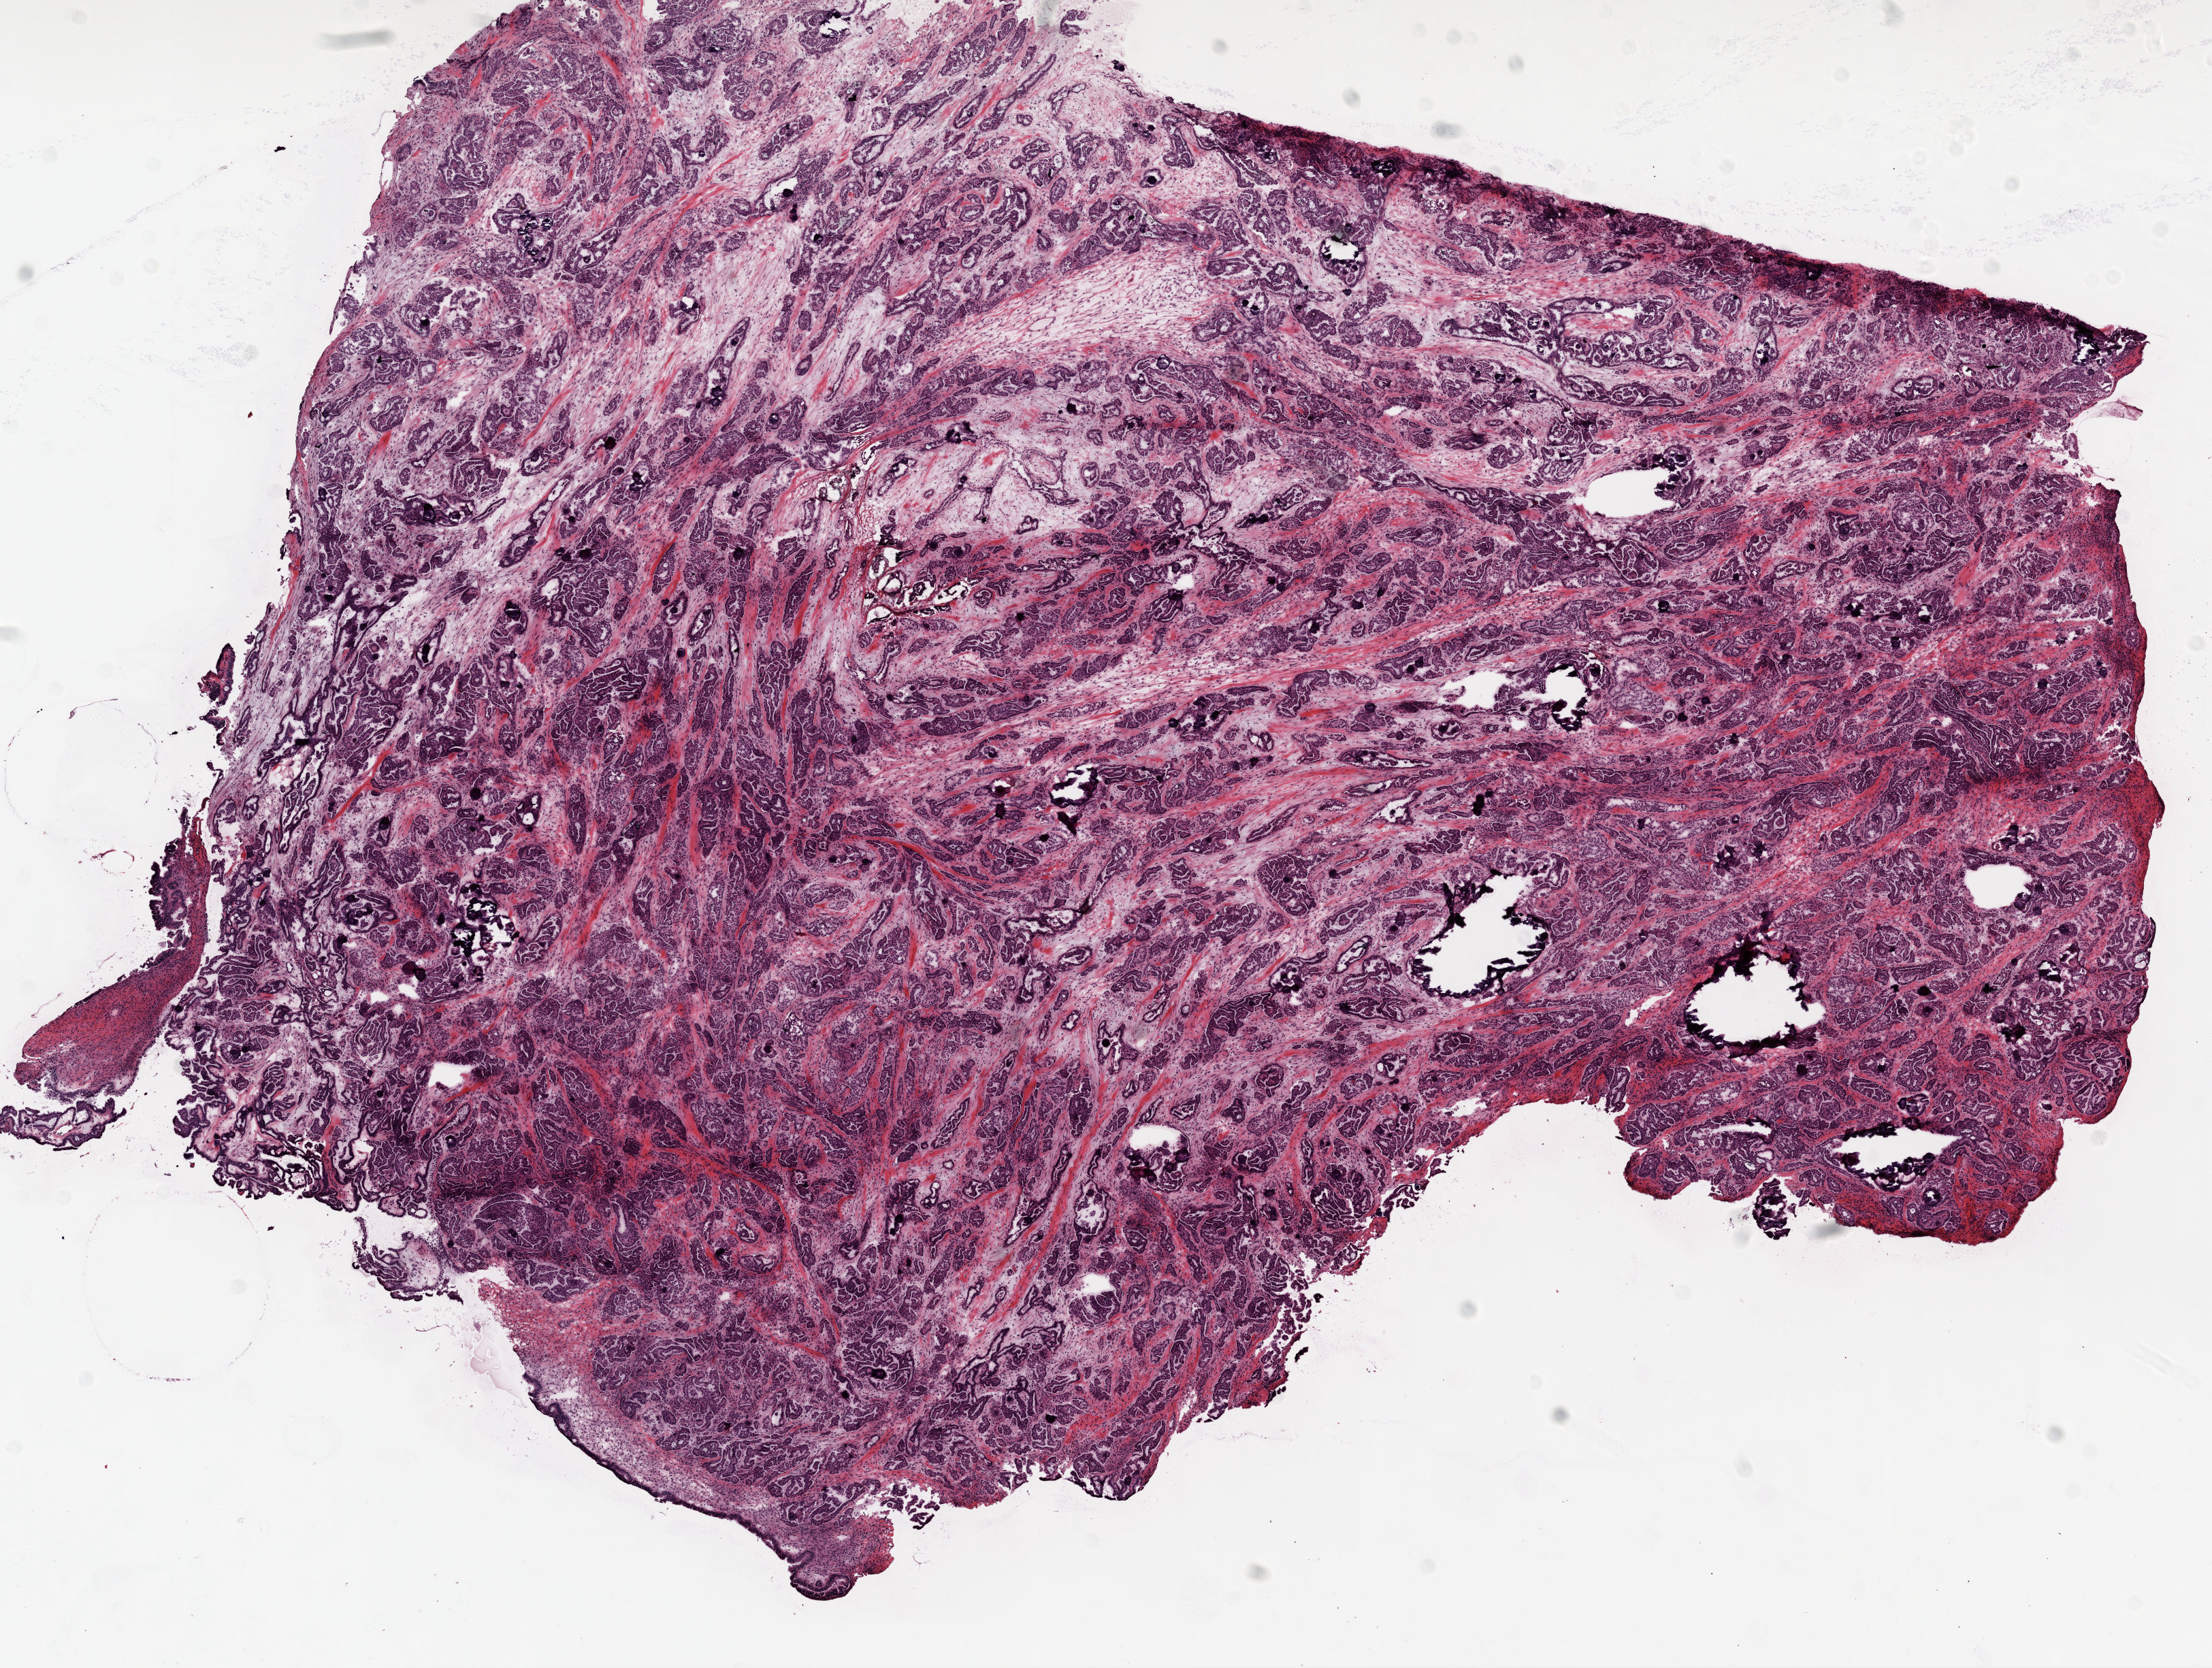
Hematoxylin and eosin (H&E) stained whole-slide image — low-resolution overview of the scanned area, about 13.0 x 9.8 mm (acquisition: 20x scan). Frozen section from the top of the tissue portion. Primary tumour sample from the ovary. Female patient; age at initial diagnosis 66 years. Histologic grade: G2 (moderately differentiated). Pathologist review of this section (percent, as recorded): tumour cells 100%, tumour nuclei 95%, normal cells 0%, stromal cells 0%, necrosis 0%. Infiltration values recorded for this section: neutrophil infiltration 1%.
- FIGO stage: IIIC
- pathologic diagnosis: Serous cystadenocarcinoma, NOS